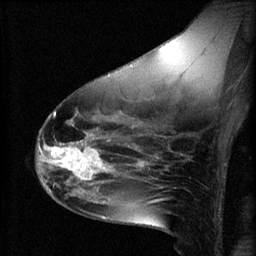
Breast MRI (dynamic contrast-enhanced), one sagittal slice; slice 36 of 60 in the series (ordered by position); 3 images stored at this slice position (order not interpretable as contrast timing); 1.5 T; TE 4.2 ms, TR 8.2 ms; 256 × 256 image matrix, field of view 180 × 180 mm. Female patient, age 49 years.
Outlined on this slice (semi-automatic segmentation, software-assisted and operator-edited):
- analysis volume of interest (the breast-tissue region the enhancement analysis was run in; not a lesion): bounding box <45,136,109,187> (left, top, right, bottom; pixels)
- tumour enhancement mask (voxels above the 70 % enhancement threshold inside the analysis volume of interest): <45,140,109,185>